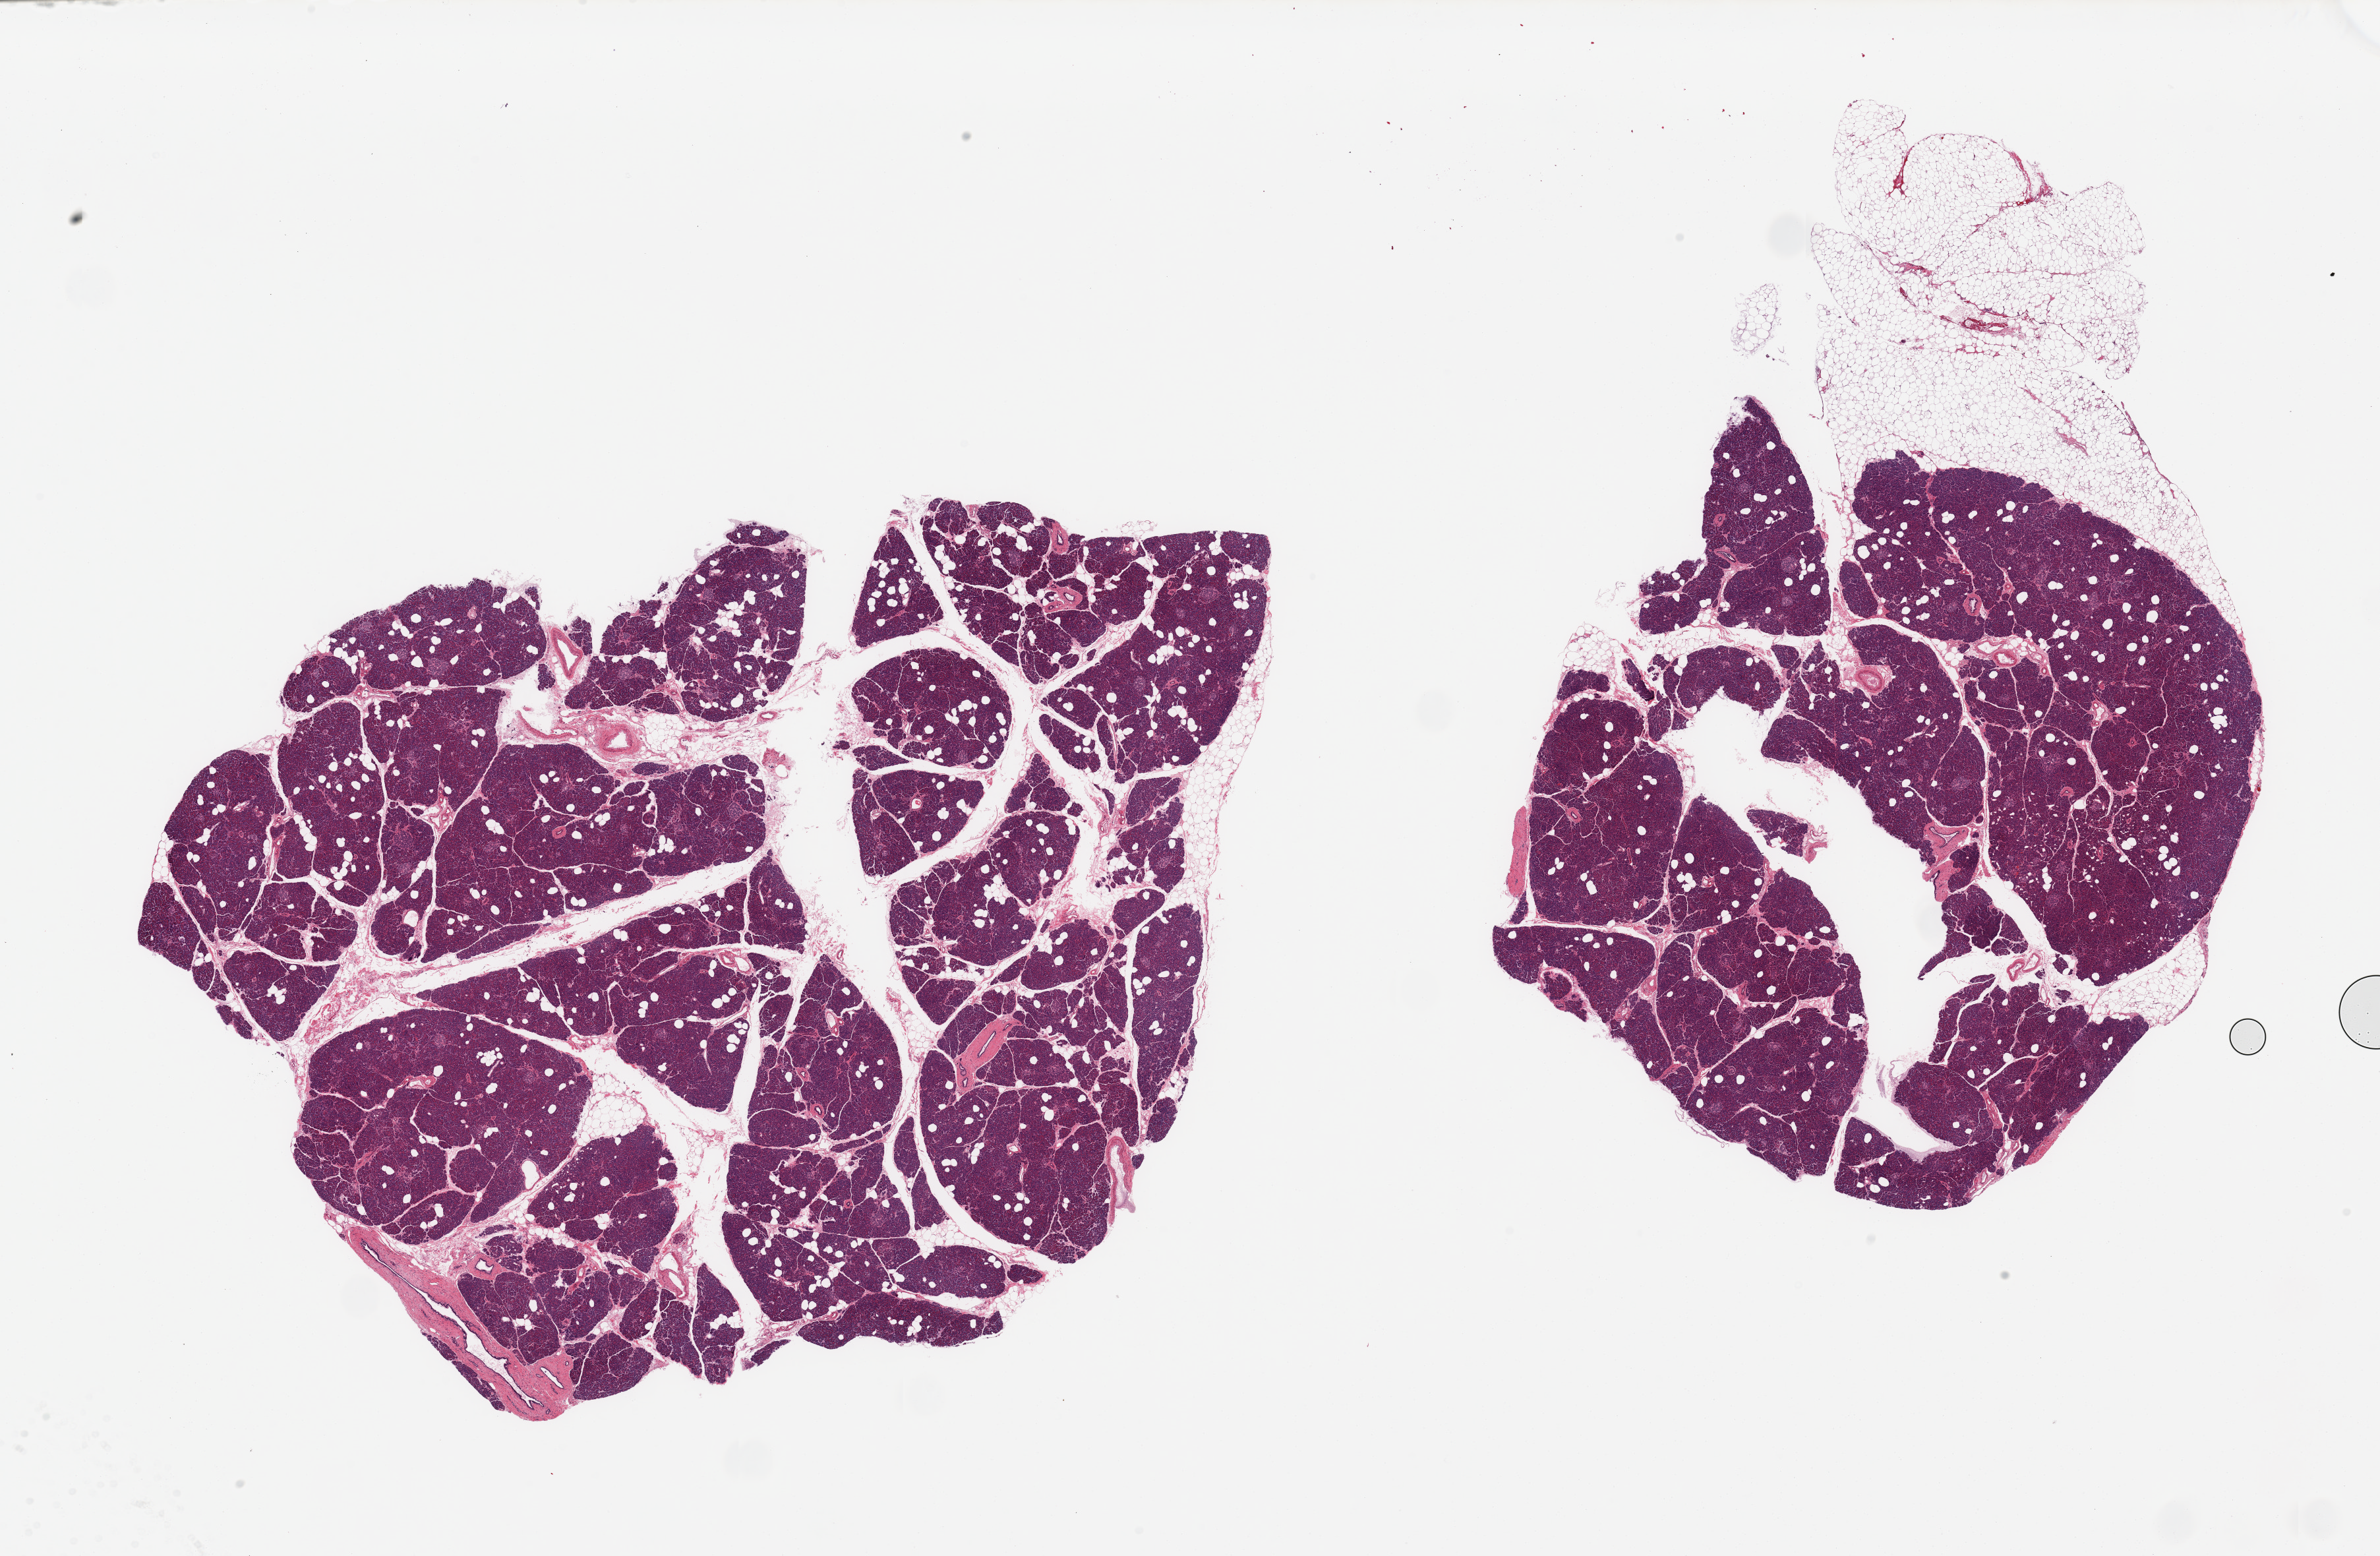
Digitized hematoxylin and eosin (H&E)-stained section — whole scanned area (about 28.5 x 18.7 mm, acquisition: 20x scan) shown as a low-resolution overview; PAXgene-fixed paraffin-embedded (PFPE) section; sampled site (target tissue): pancreas; tissue donor sample. Donor sex: female.
• review note (as recorded): 2 pieces; 1 piece has 25% external fat; both have 5% internal fat